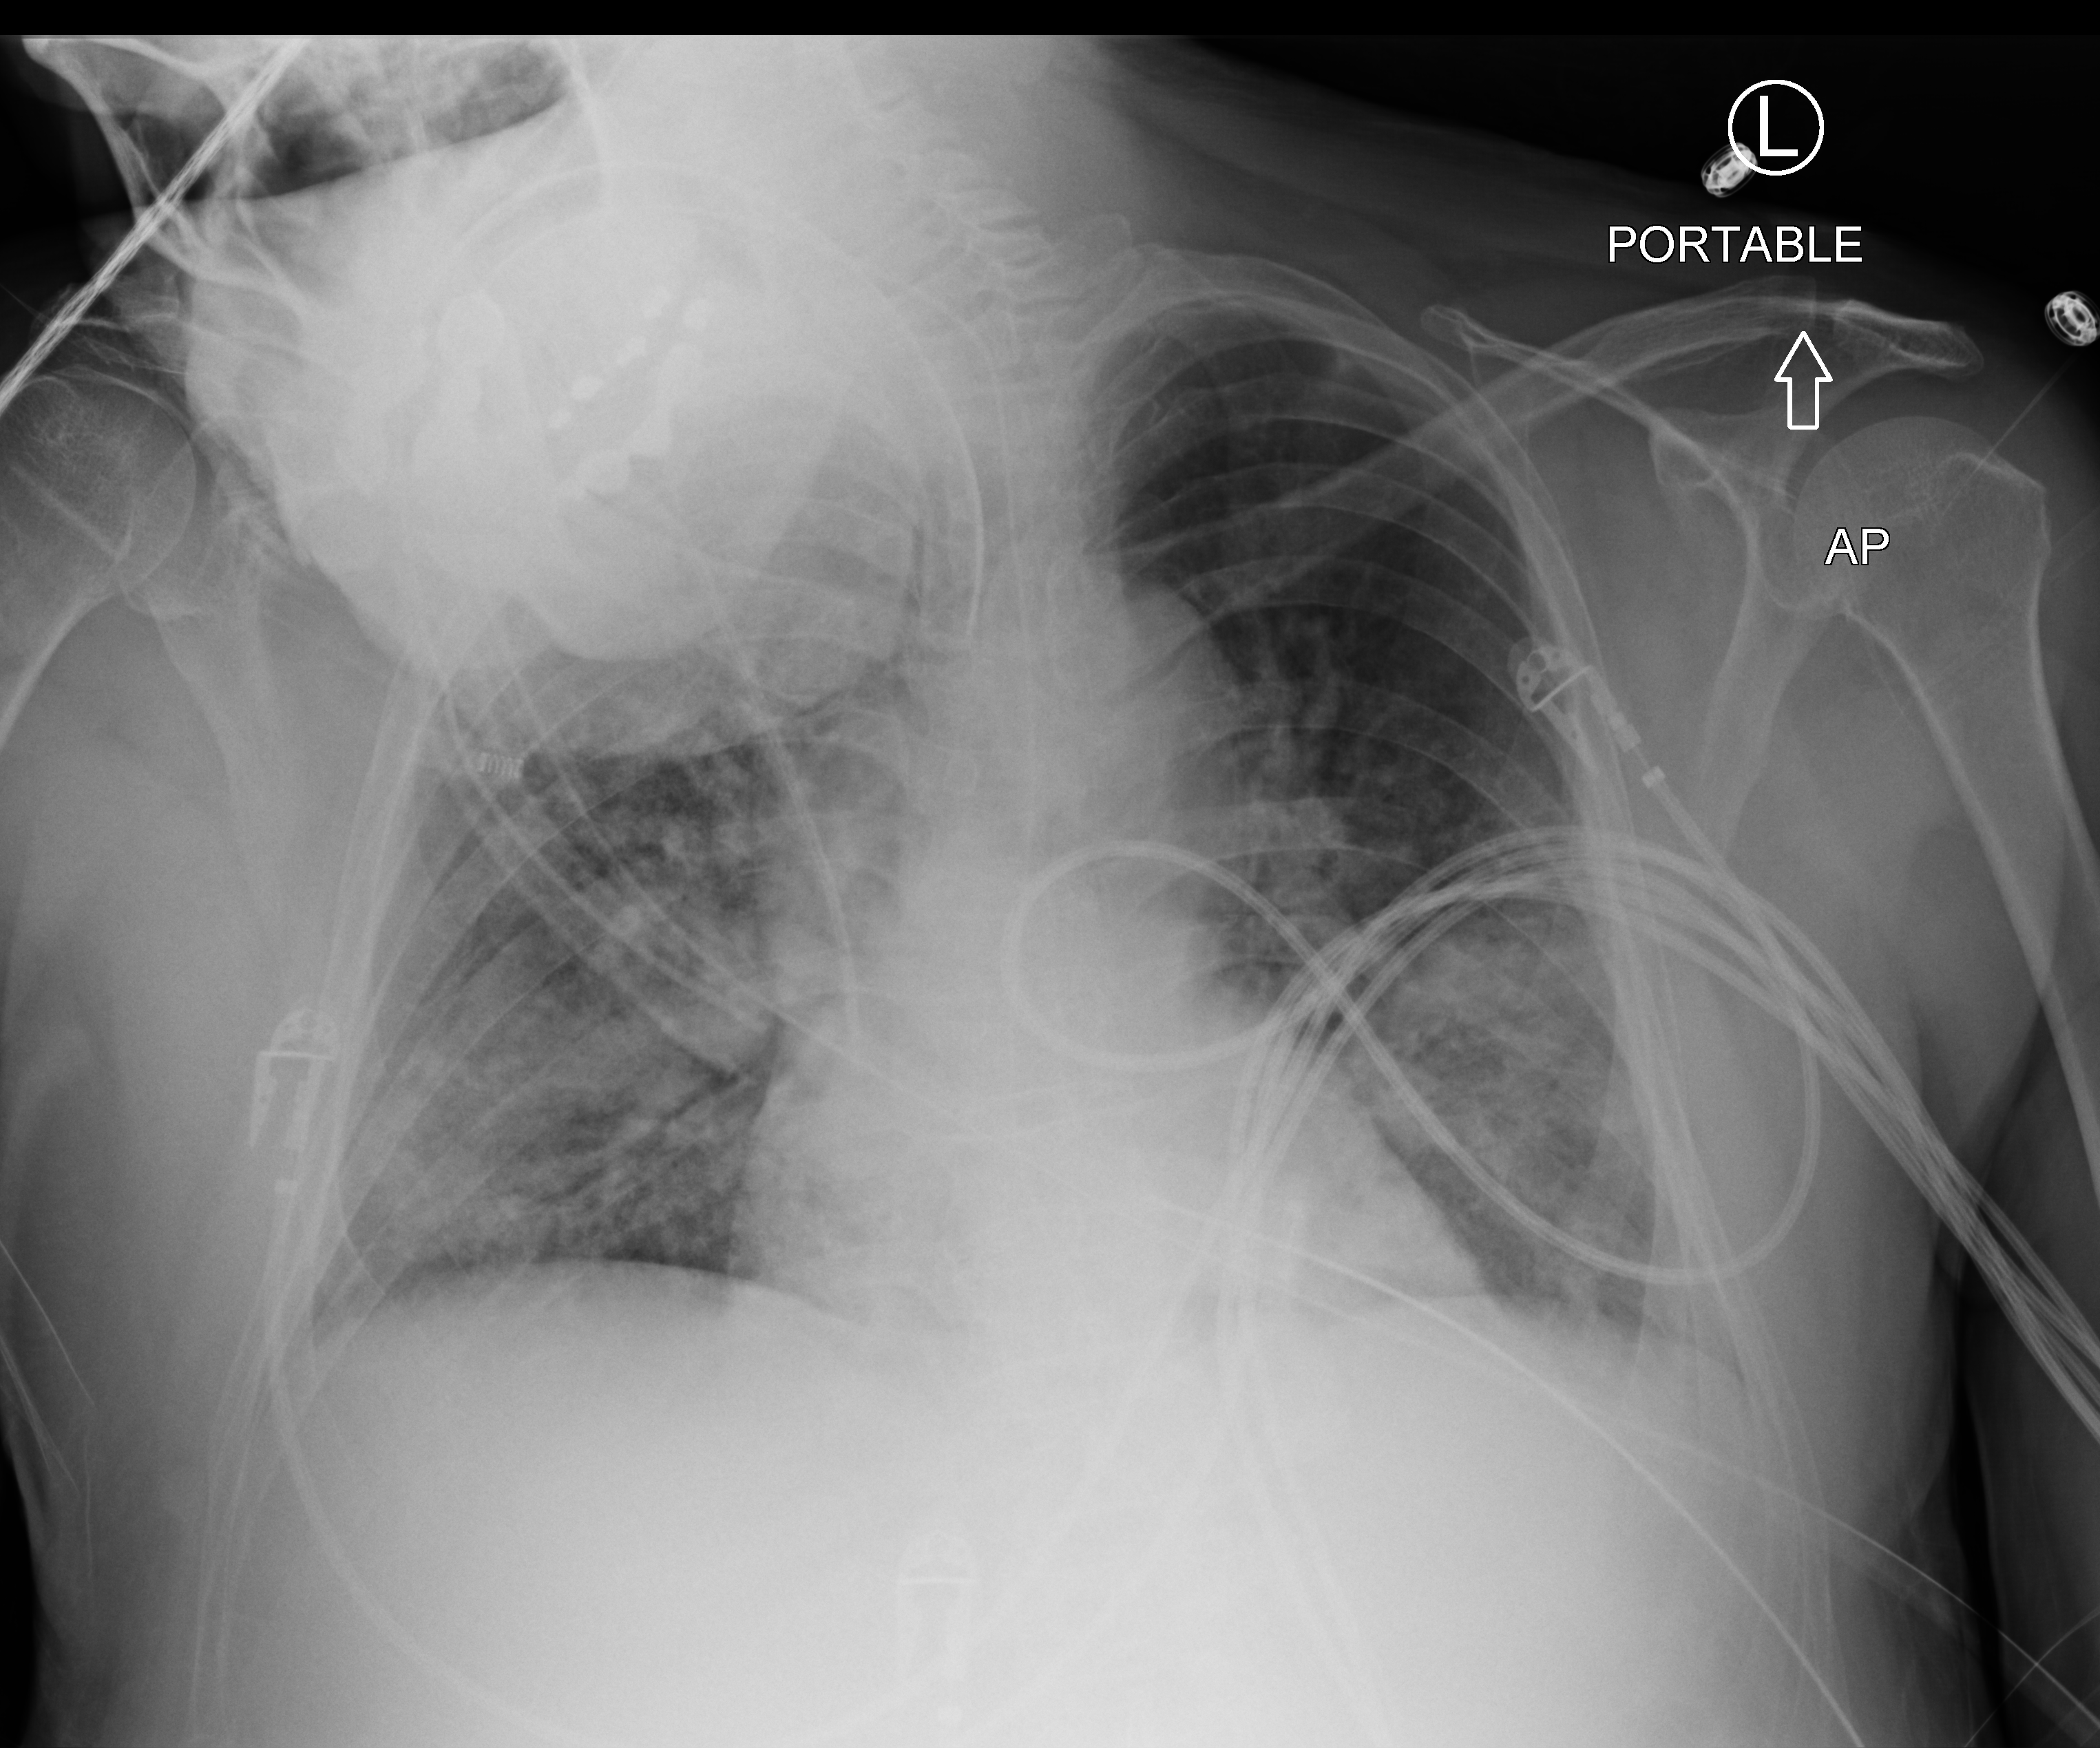
Bedside chest radiograph (computed radiography), anteroposterior (AP) projection. Male patient hospitalised with COVID-19, age 60–74 years.
Hospital-stay facts (about this admission, not read from this image; timing relative to this image not recorded):
- chronic kidney disease (admission record): no